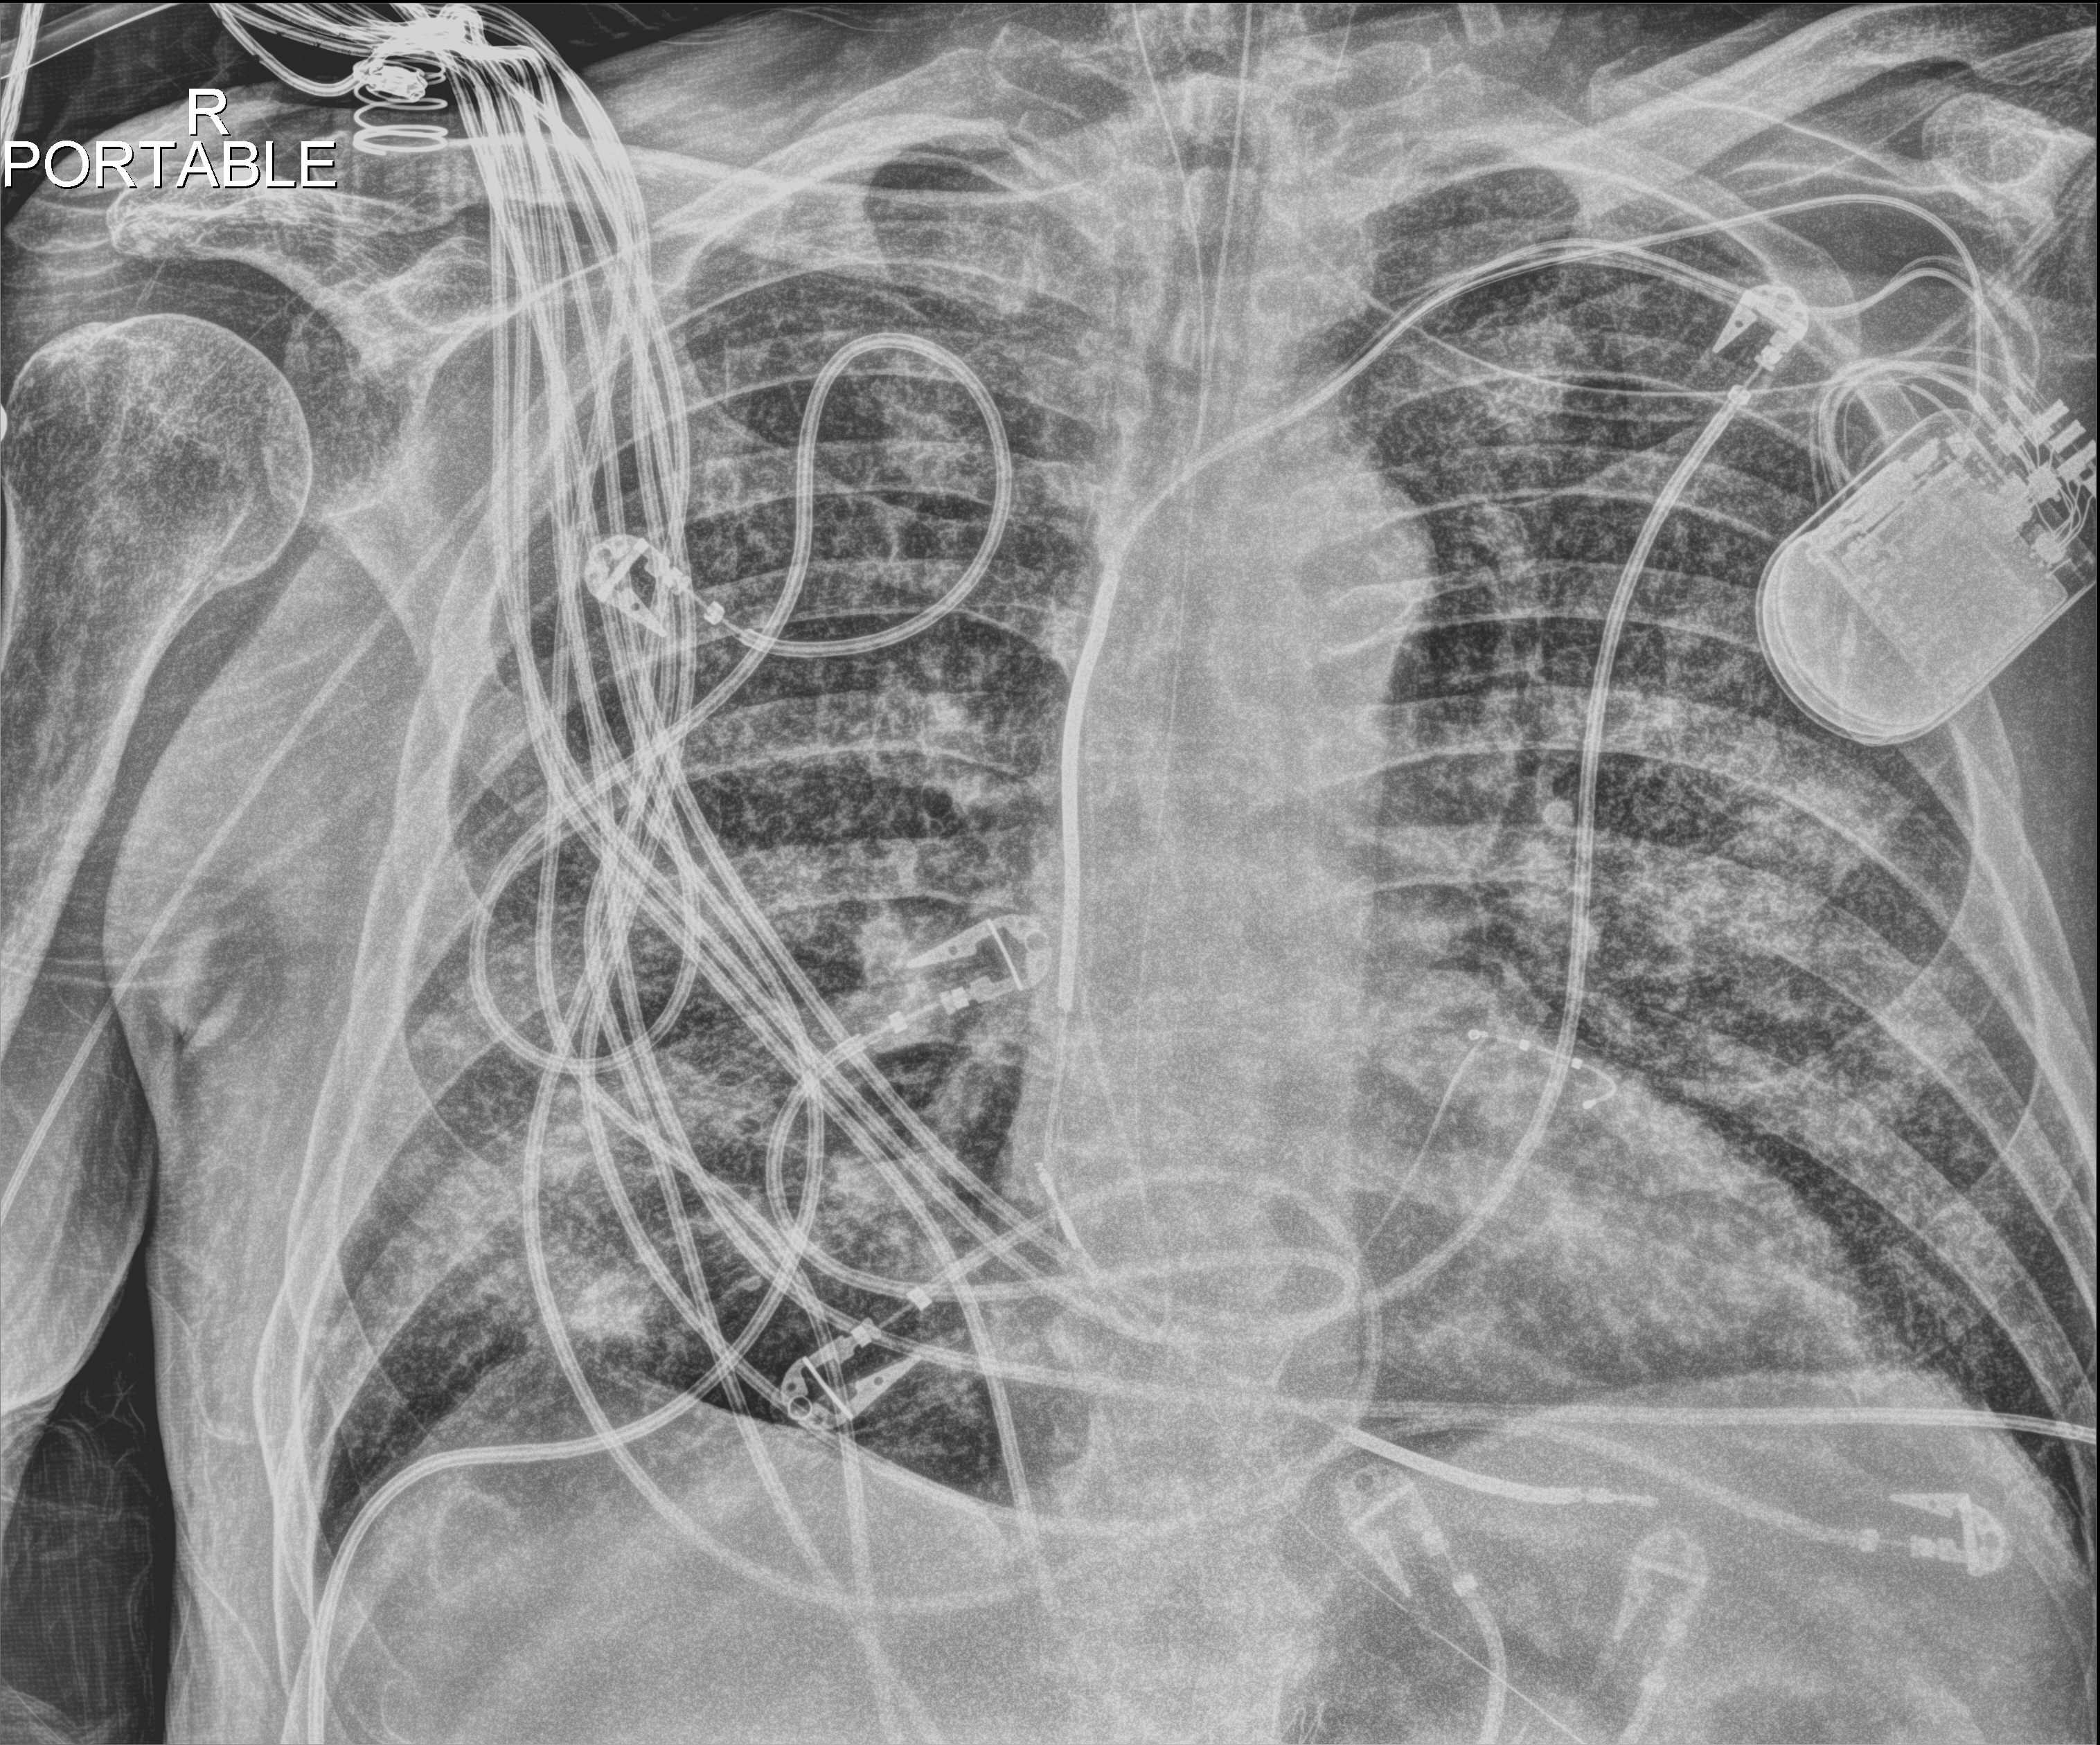
Chest X-ray (portable), anteroposterior (AP) projection. Male patient hospitalised with COVID-19, age 60–74 years.
From the hospital-stay record, not from the radiograph (when in the stay this image was taken is not recorded): length of hospital stay: 36 days.